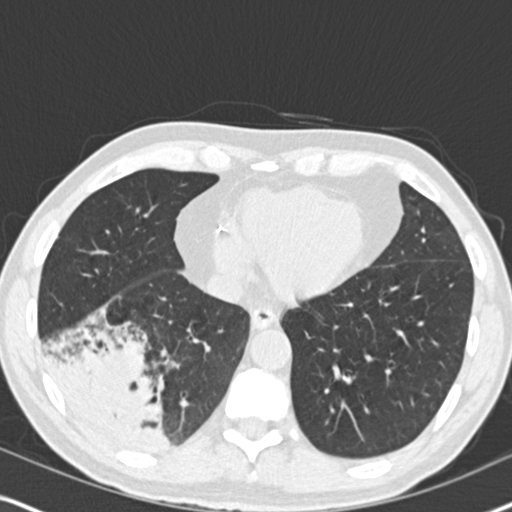
Low-dose screening chest CT, axial slice, second screening round (one year after baseline), lung window (W 1500 / L -600 HU), 2 mm slice thickness, standard (soft-tissue) reconstruction kernel (B30f), slice 117 of 182 in the series. Male participant, aged 61 years at enrolment. Current smoker at enrolment.
Lesion marked by an expert reader, bounding box [x1, y1, x2, y2] px = [38, 308, 186, 460]. Reader record for this screening exam (exam-level; its link to the box is not recorded): non-calcified nodule or mass ≥4 mm, right lower lobe, 90 × 80 mm, soft tissue attenuation, pre-existing on the prior screen: yes; interval growth: yes. Official screen result: positive, other. Participant outcome: lung cancer diagnosed 20 days after this screen — bronchiolo-alveolar adenocarcinoma, NOS, right lower lobe, moderately differentiated (G2), stage IIIB (AJCC 6th edition), 90 mm at pathology.